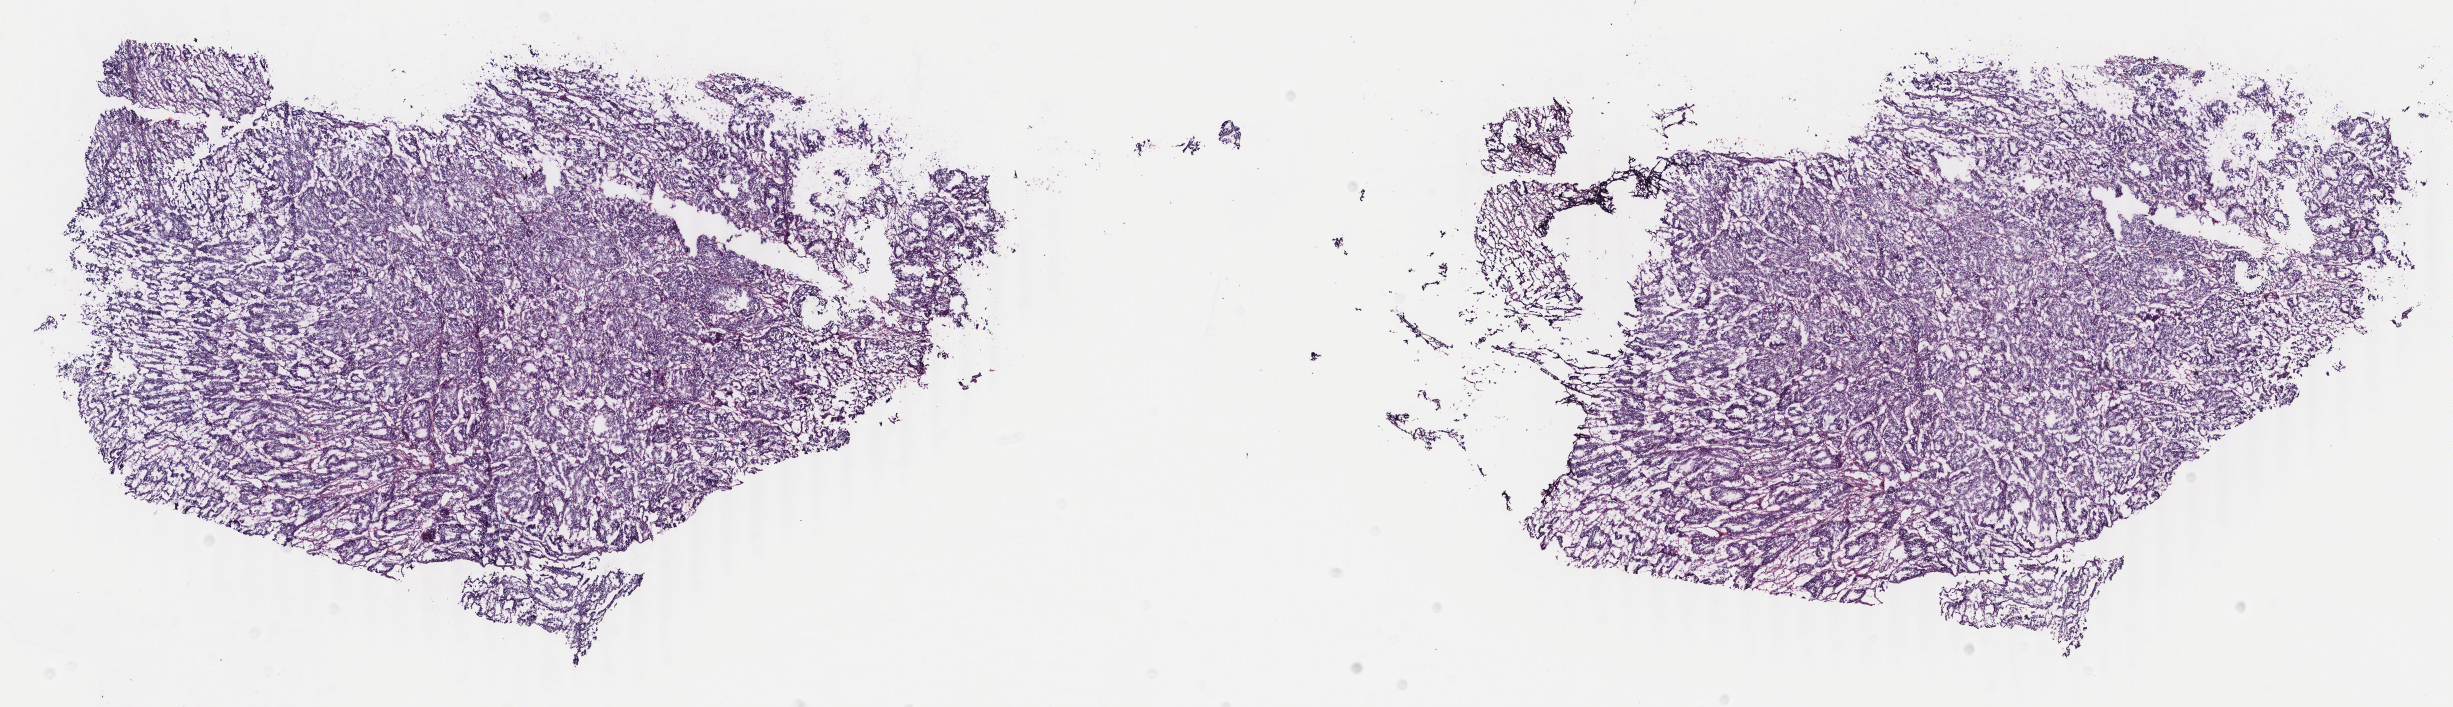
Digitized H&E-stained tissue section (whole slide) — shown as a low-resolution overview of the whole scanned area (about 19.5 x 5.6 mm). Frozen section from the top of the tissue portion. Uterus, primary tumour sample. Female, age 45 years at initial diagnosis. Histologic grade: G2 (moderately differentiated). Composition of this section per pathologist review: tumour cells 100%, tumour nuclei 90%, normal cells 0%, stromal cells 0%, necrosis 0%. Inflammatory infiltration, as recorded: lymphocyte infiltration 0%, monocyte infiltration 0%, neutrophil infiltration 0%.
FIGO stage: IA. Pathologic diagnosis: Endometrioid adenocarcinoma, NOS.